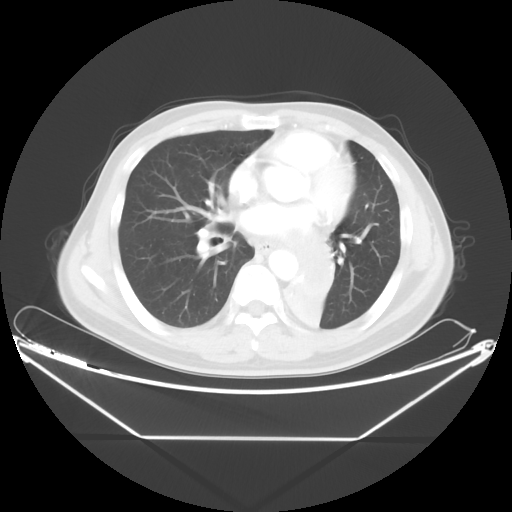
Chest CT, one axial slice; position 21 of 48 along the scan axis; reconstruction kernel STANDARD; lung window (W 1500 / L -600 HU); 5 mm slice thickness; 512 × 512 image matrix, field of view 438 × 438 mm. Patient: male, 58 years. Case-level facts recorded for this patient, not image findings: clinical TNM (as recorded): T3 N3 M0.
Annotated regions visible in this slice (rectangle marked by the reading radiologist):
- lung tumour (recorded histology: squamous cell carcinoma): box from (x=284, y=229) to (x=380, y=347) px